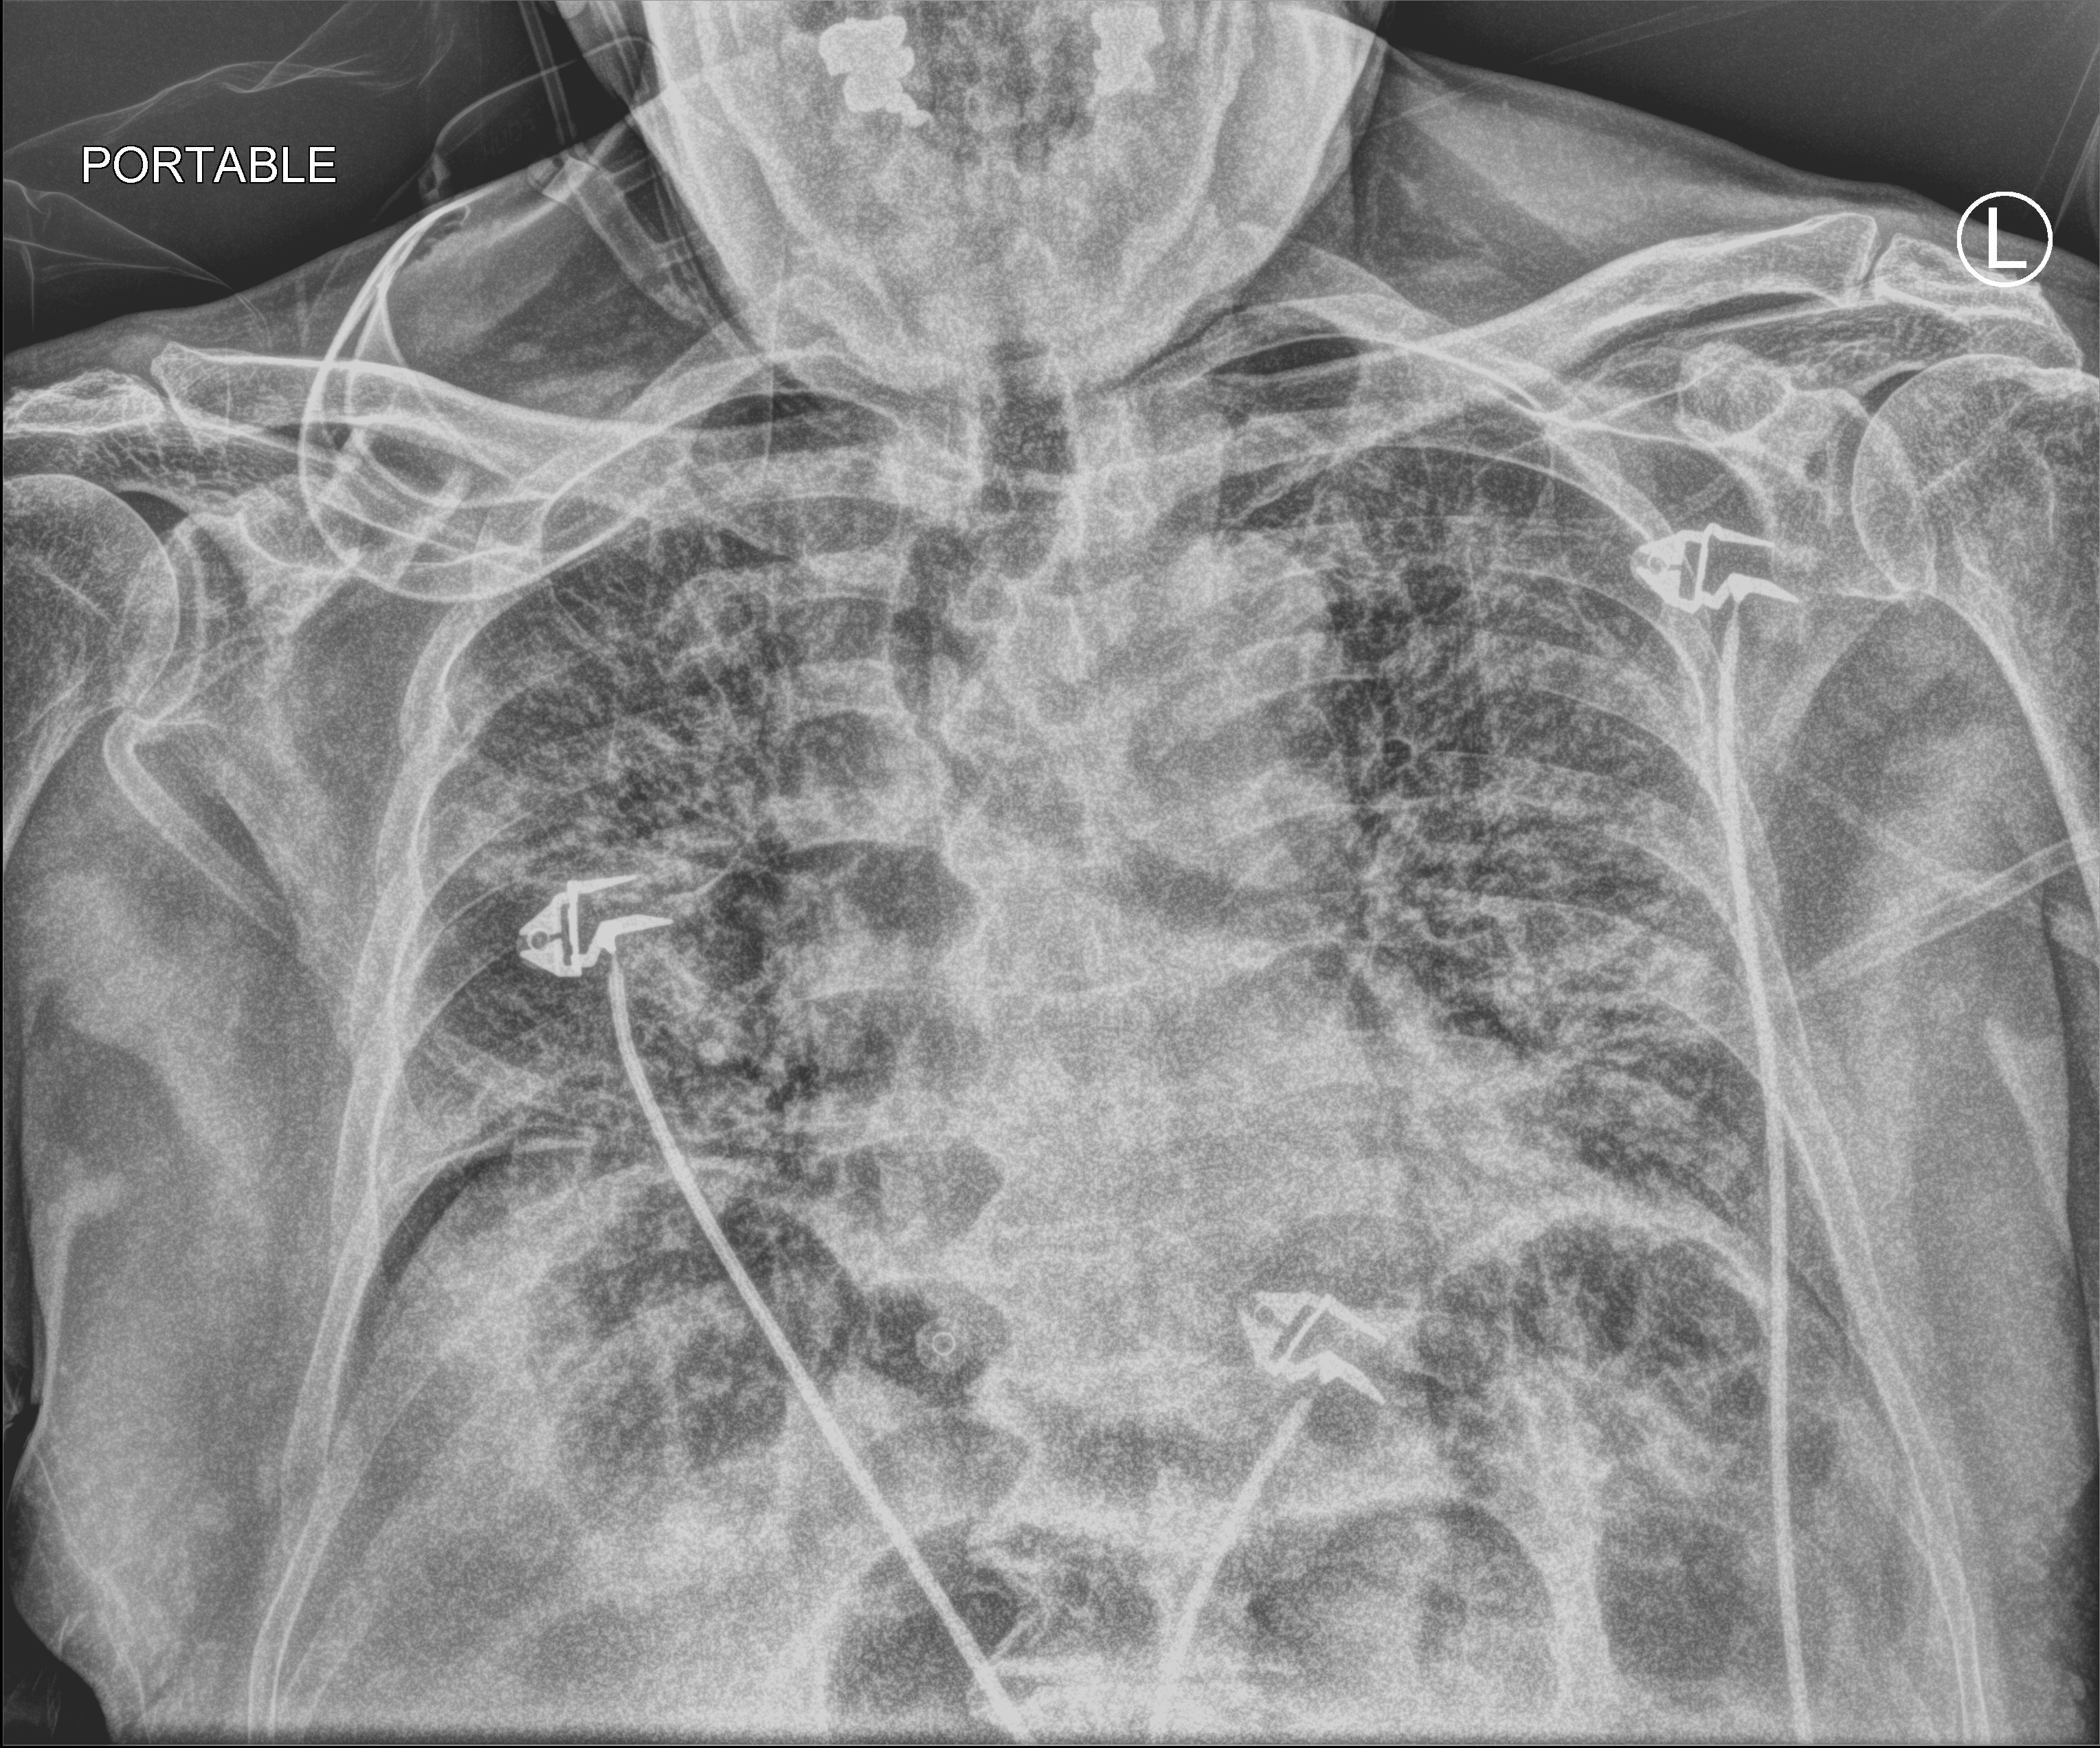
Bedside chest radiograph (computed radiography). Male patient hospitalised with COVID-19, age 75–90 years.
Hospital-stay facts (about this admission, not read from this image; timing relative to this image not recorded): smoking status (admission record): former.